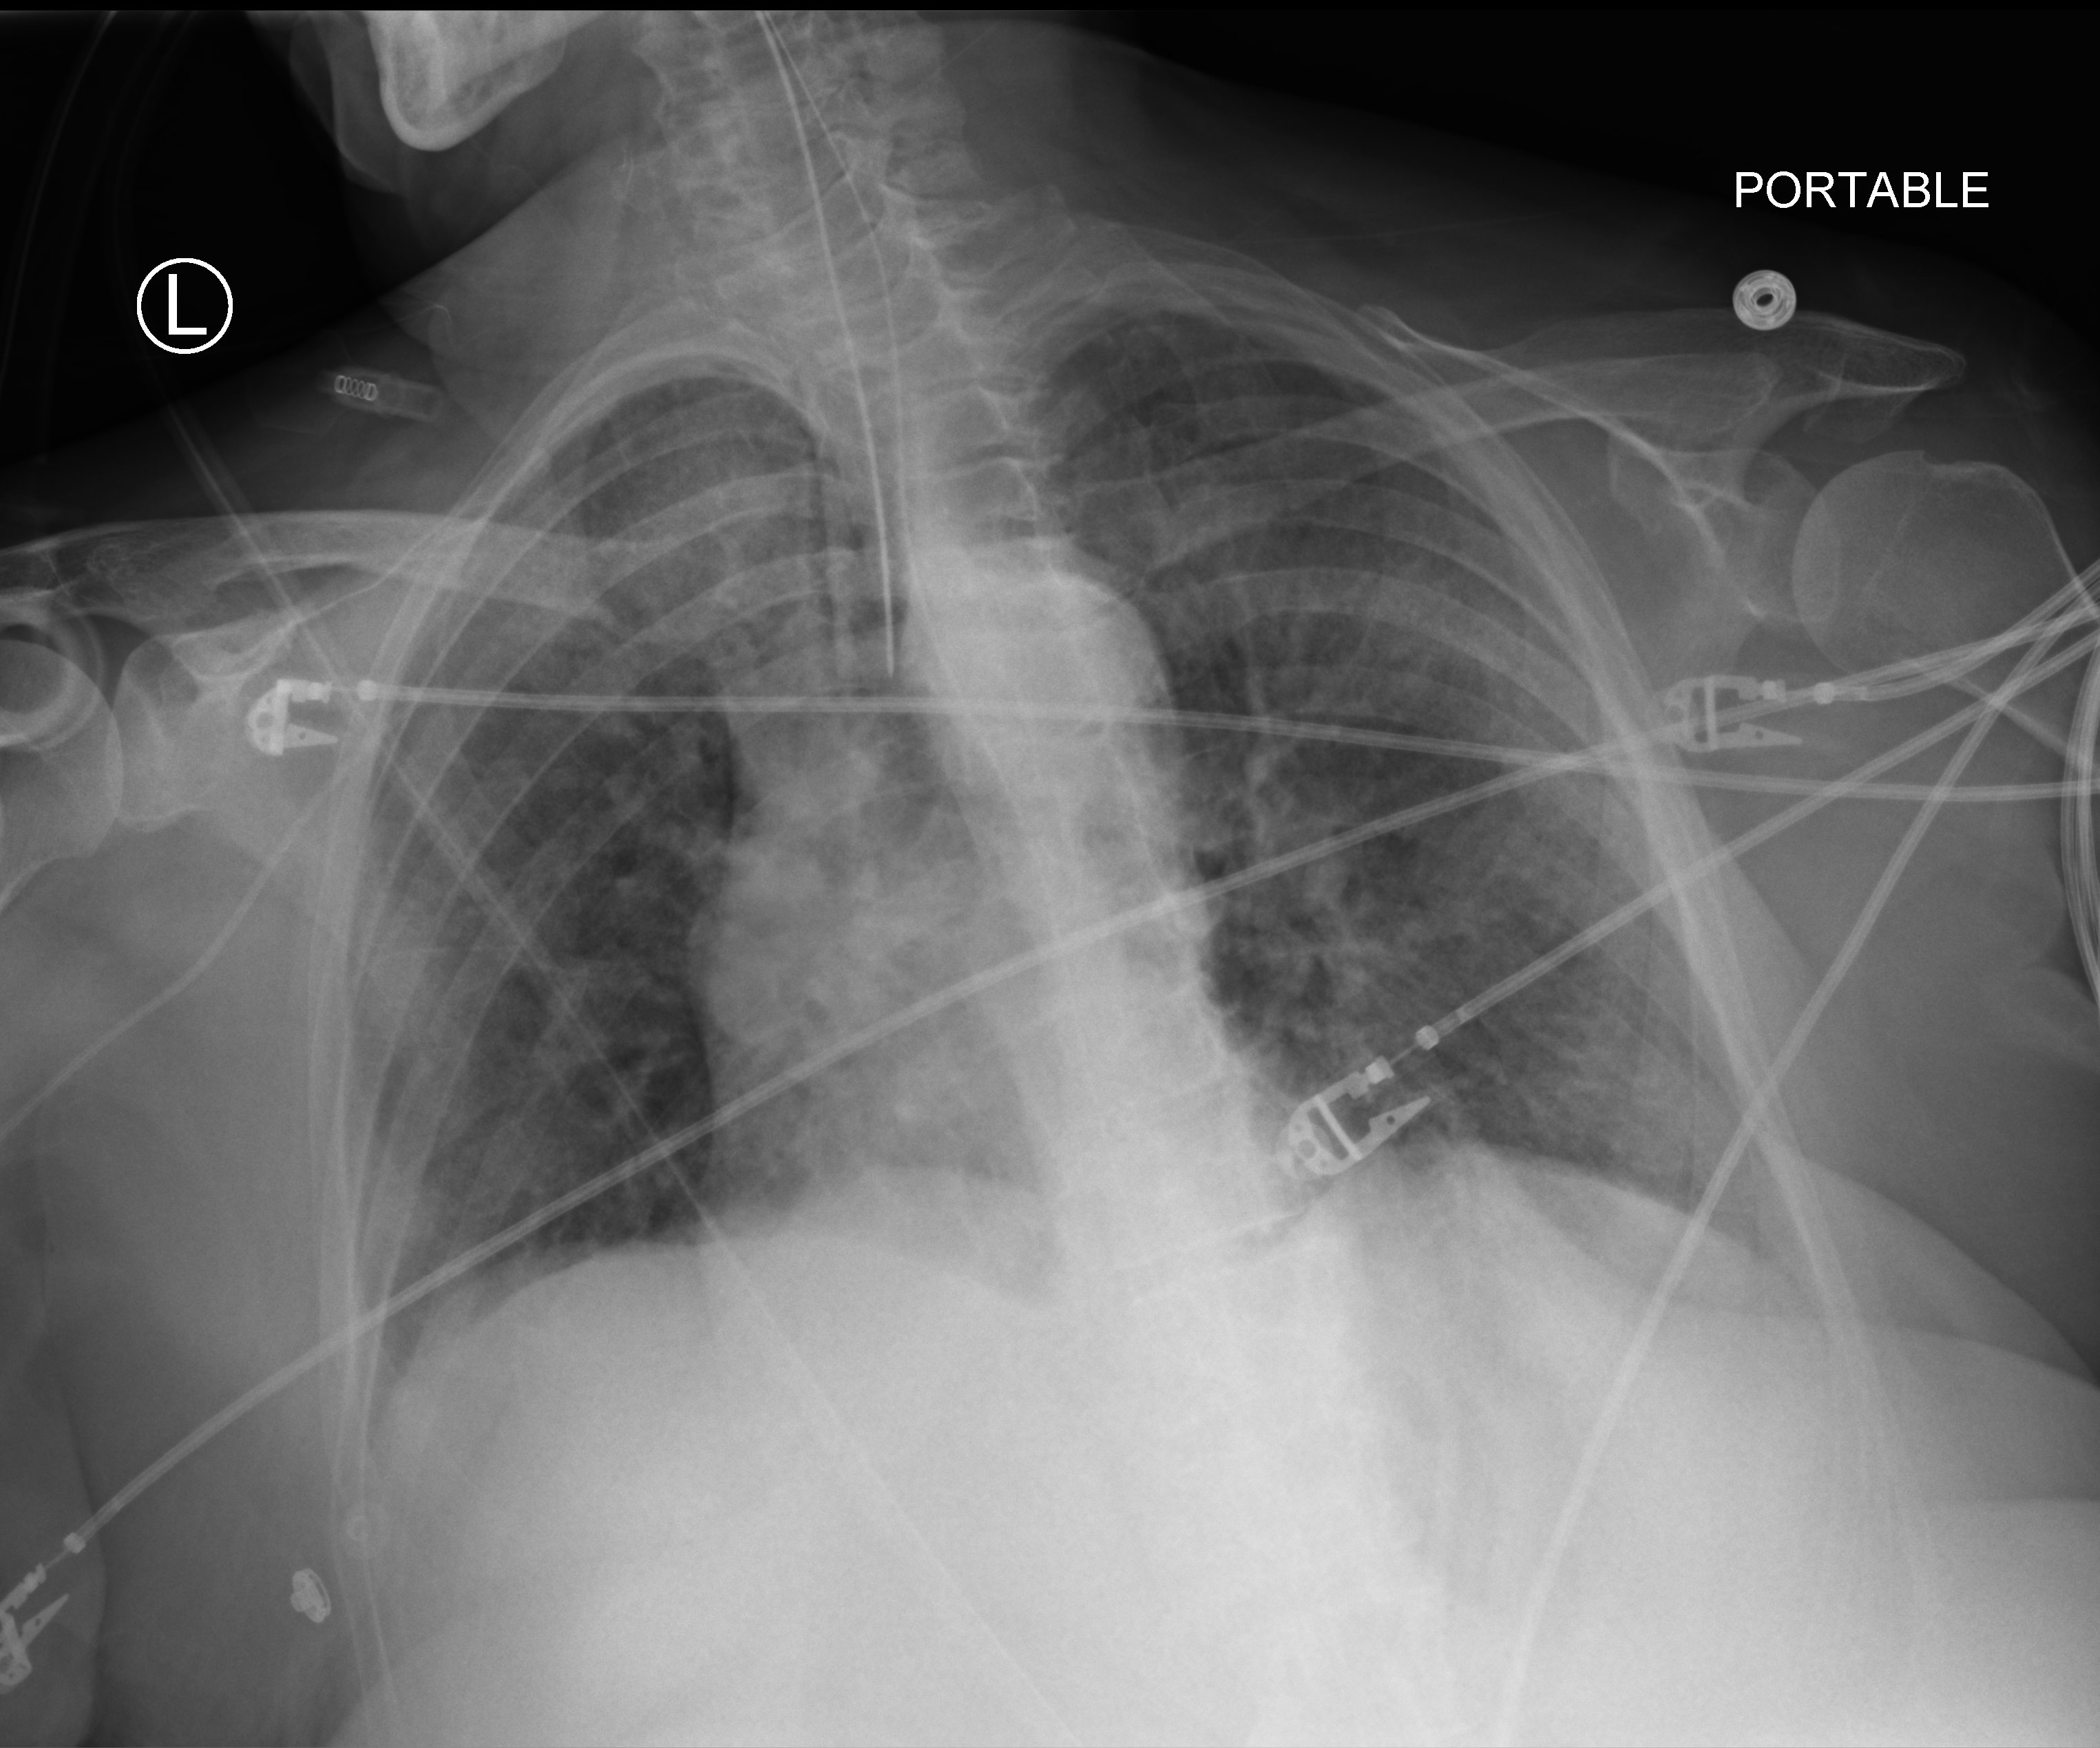
Chest X-ray (portable), anteroposterior (AP) projection. Female patient hospitalised with COVID-19, age 75–90 years.
From the hospital-stay record, not from the radiograph (when in the stay this image was taken is not recorded): hypertension (admission record): yes; admitted to intensive care during this hospital stay: yes.